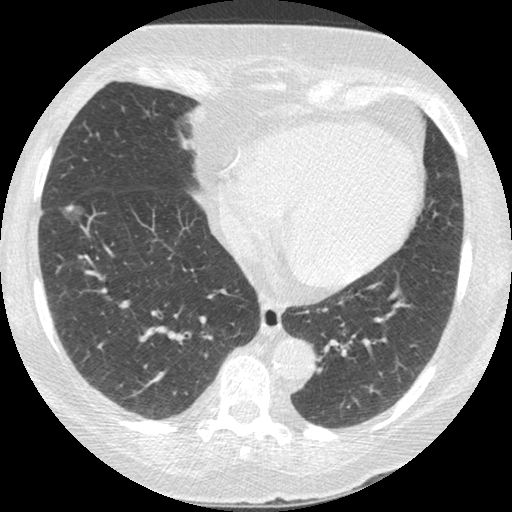
Low-dose screening chest CT, one axial slice; position 96 of 245 along the scan axis; reconstruction kernel STANDARD; lung window (W 1500 / L -600 HU); 1.25 mm slice thickness; 512 × 512 image matrix, field of view 310 × 310 mm.
Outlined on this slice (expert manual segmentation):
- lesion 1 (tumor, lower lobe of right lung): bounding box (x1, y1, x2, y2) in pixels: (65, 205, 78, 215)